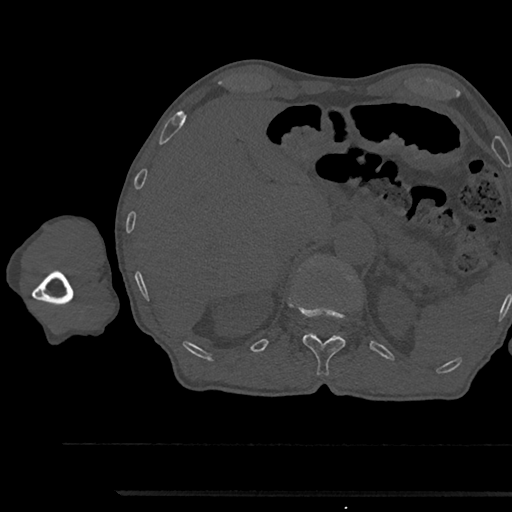
CT including the spine, one axial slice. Slice 694 of 797 in the series (ordered by position). Reconstruction kernel Br40s/3. Bone window (W 1800 / L 400 HU). 0.5 mm slice thickness. 512 × 512 image matrix, field of view 367 × 367 mm. Male patient, age 79 years. Case-level facts recorded for this patient, not image findings: primary cancer: prostate.
Annotated regions visible in this slice (semi-automatic segmentation, software-assisted and operator-edited):
- T12 vertebra: box from (x=301, y=309) to (x=346, y=376) px